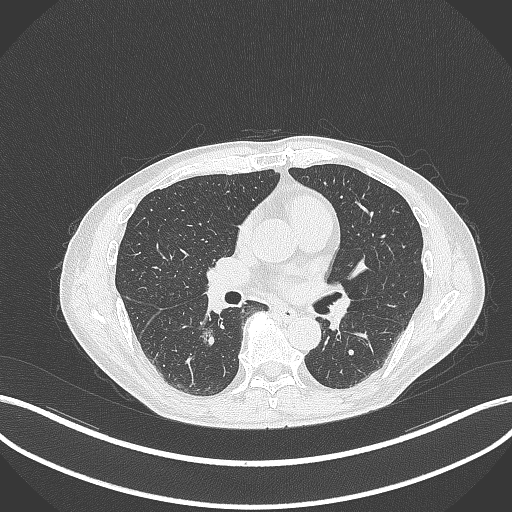
Chest CT, one axial slice. Position 165 of 323 along the scan axis. Reconstruction kernel B70f. 120 kVp. Lung window (W 1500 / L -600 HU). 1 mm slice thickness. 512 × 512 image matrix, field of view 400 × 400 mm. Patient: male, 61 years. From the clinical record (not read from this slice): clinical TNM (as recorded): T1c N0 M0.
Structures marked on this image (rectangle marked by the reading radiologist):
- lung tumour (recorded histology: adenocarcinoma): bounding box [x1, y1, x2, y2] px = [200, 328, 216, 345]